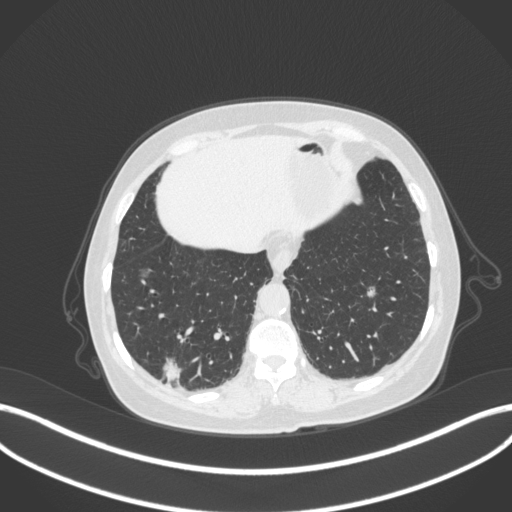
Chest CT, one axial slice; slice 66 of 340 in the series (ordered by position); 120 kVp; lung window (W 1500 / L -600 HU); 512 × 512 image matrix, field of view 400 × 400 mm. Female patient, age 69 years. Case-level facts recorded for this patient, not image findings: clinical TNM (as recorded): T1b N0 M0; histopathological grade: G2-3.
Structures marked on this image (rectangle marked by the reading radiologist):
- lung tumour (recorded histology: adenocarcinoma): bounding box [x1, y1, x2, y2] px = [160, 355, 184, 380]